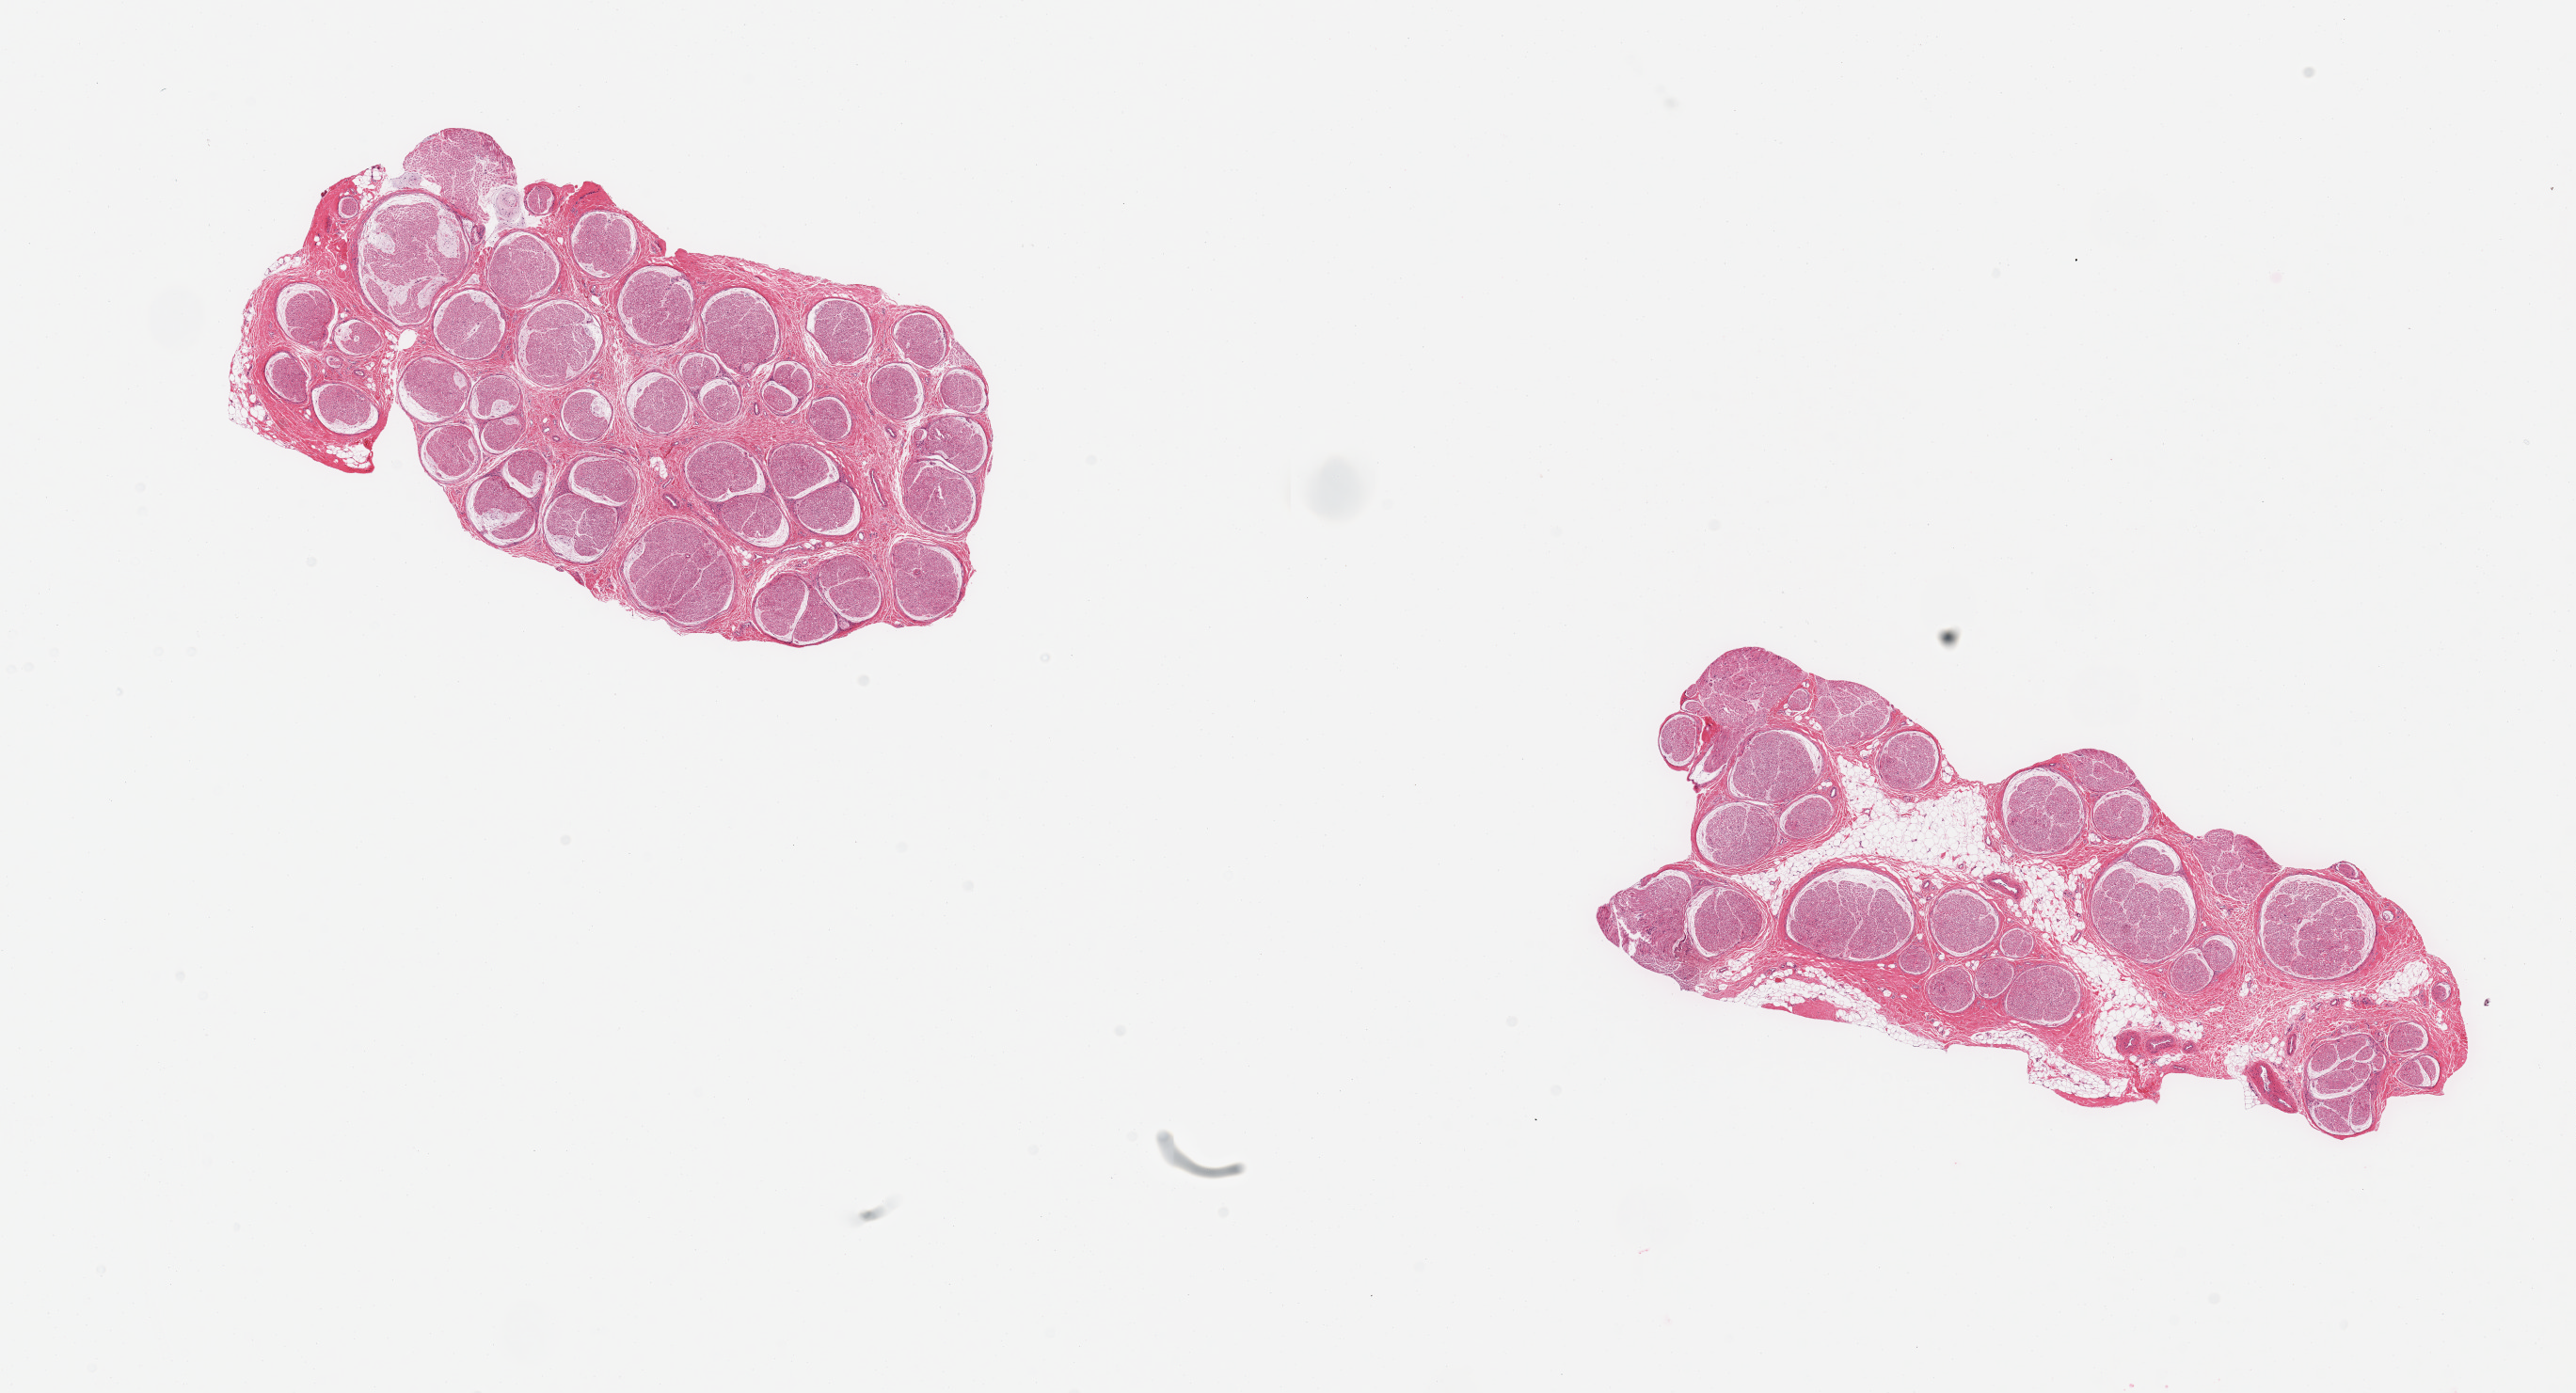
Hematoxylin and eosin (H&E) whole-slide image, brightfield, shown as a low-resolution overview of the whole scanned area (about 21.7 x 11.7 mm, acquisition: 20x scan); PAXgene-fixed, paraffin-embedded tissue; target tissue: tibial nerve; donor tissue sample. Male donor.
Review note (as recorded): 2 pieces, excellent clean specimen.